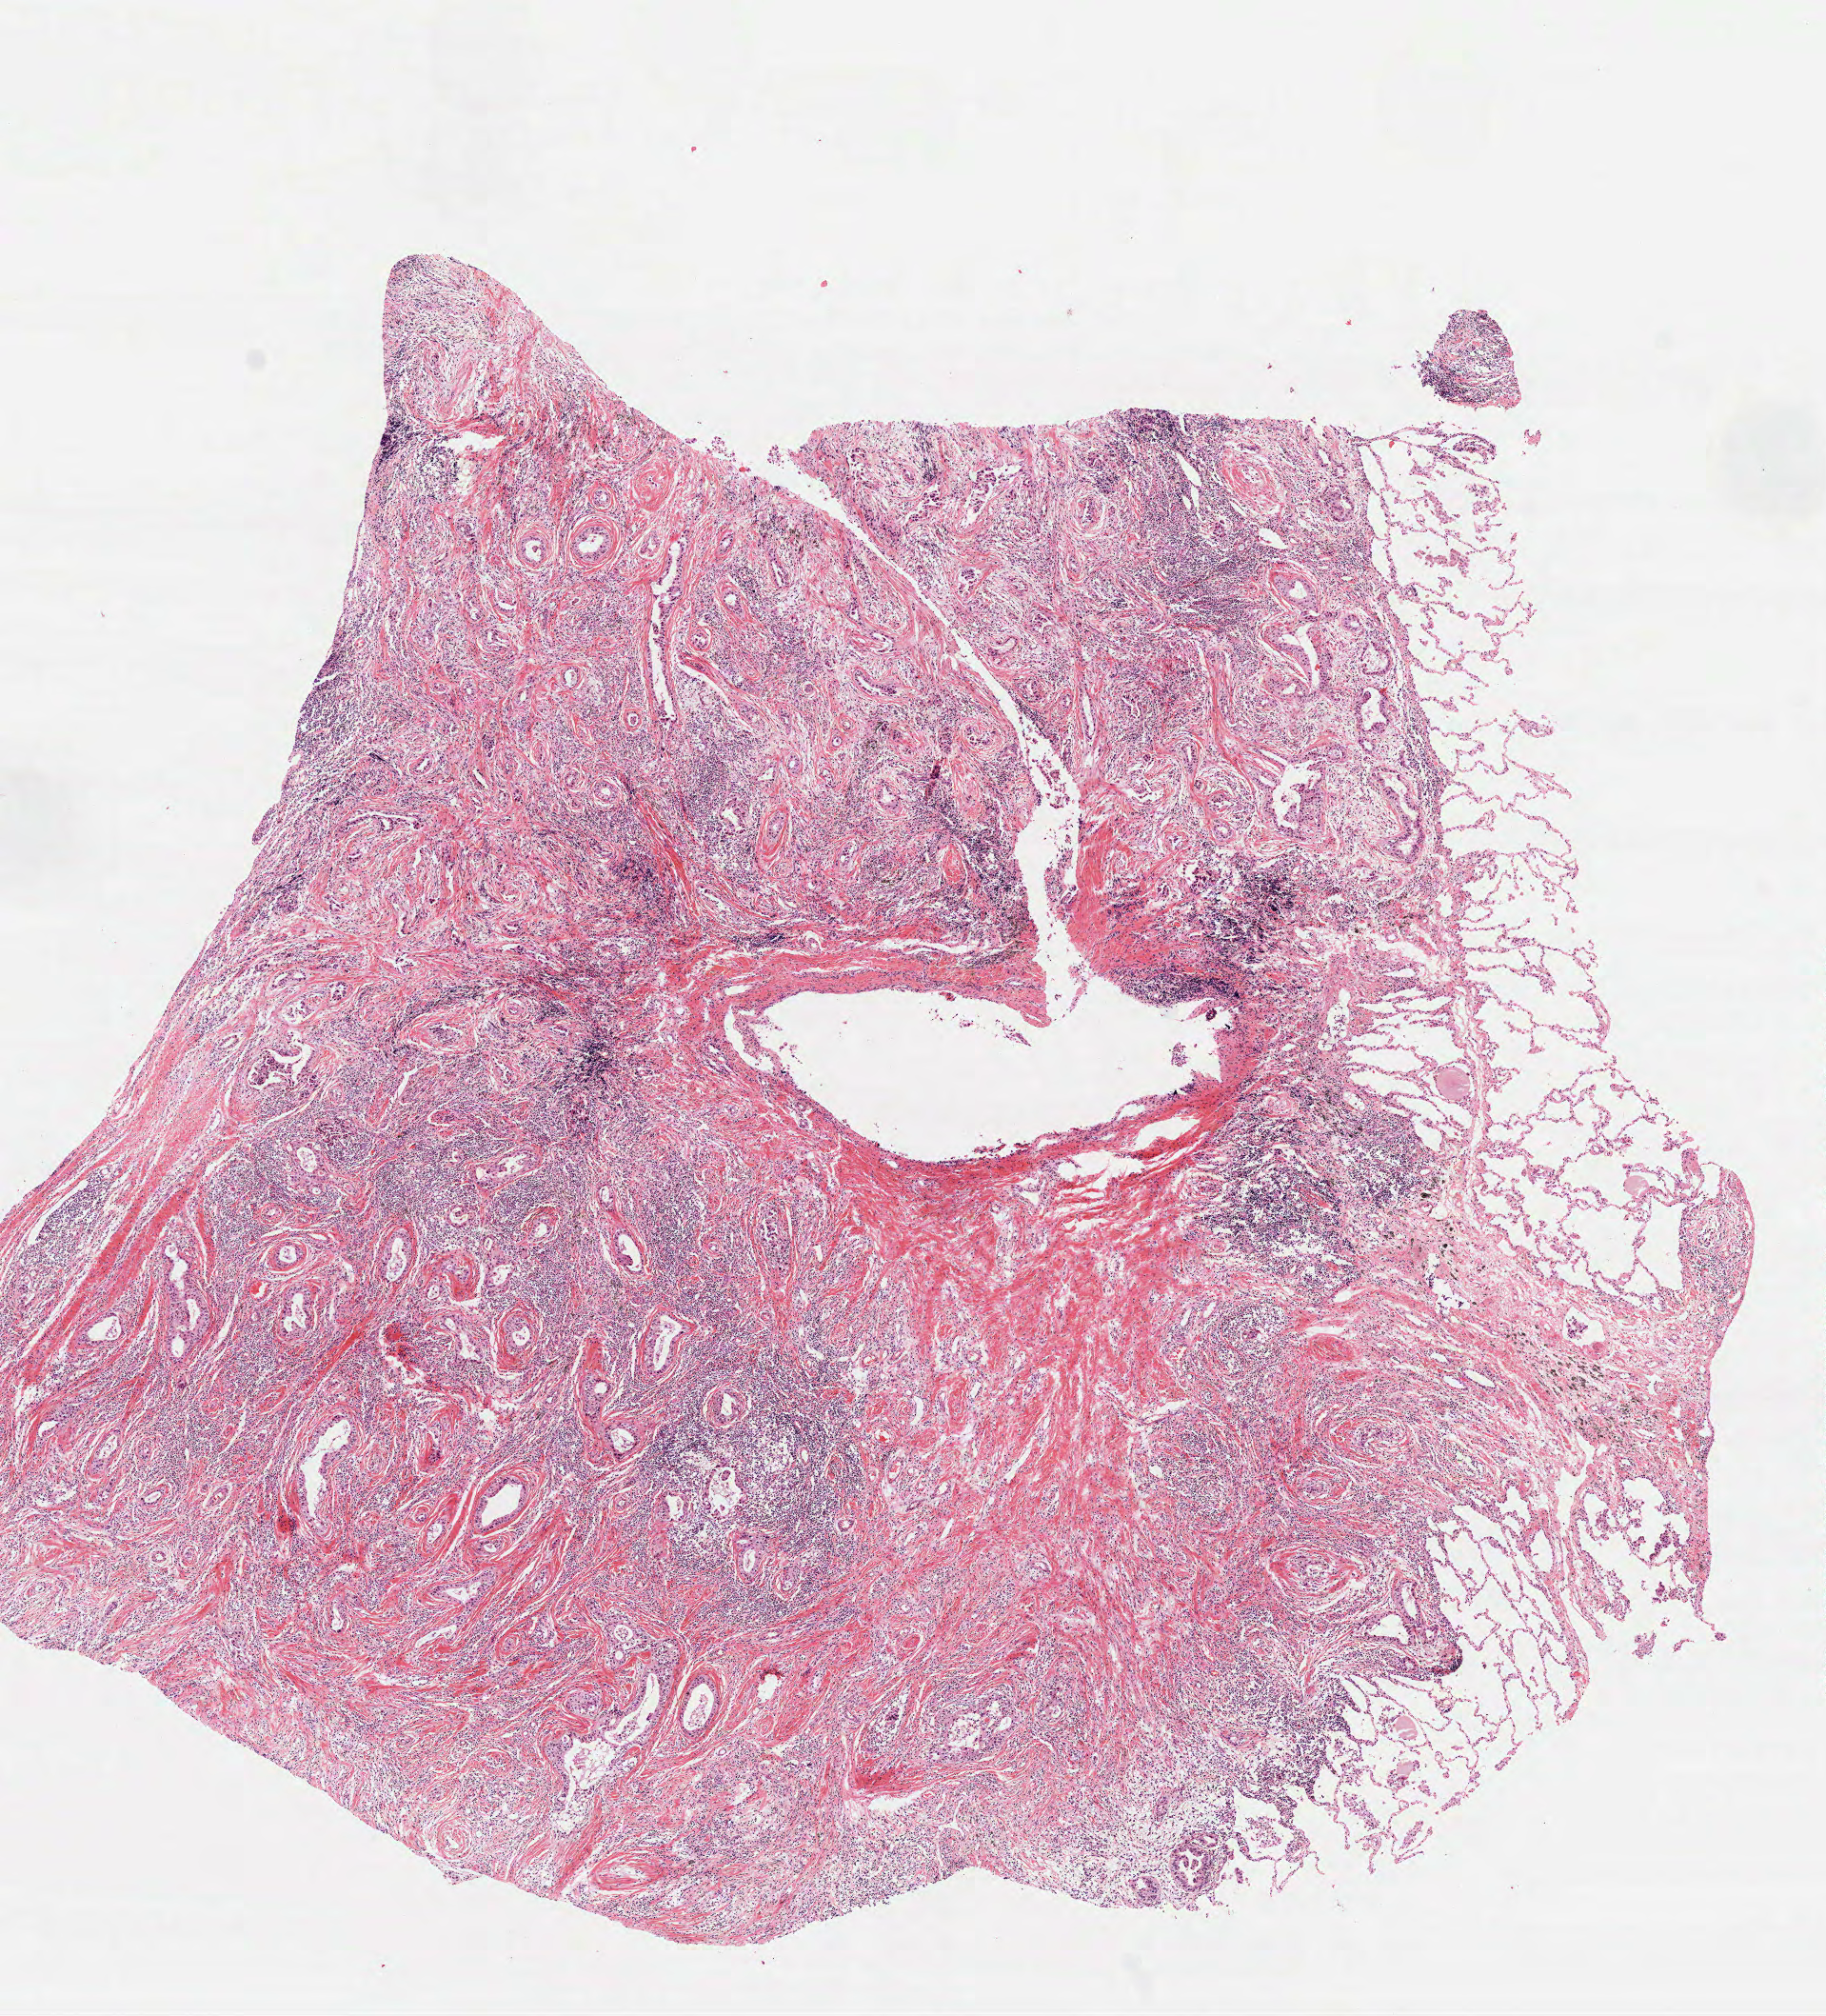
H&E whole-slide image — a low-resolution overview of the entire scanned area, about 7.7 x 8.5 mm; formalin-fixed paraffin-embedded (FFPE) diagnostic section; lung, primary tumour sample. Patient: female, age at initial diagnosis 72 years.
* AJCC pathologic stage: IIB (7th edition)
* laterality: right
* TNM: T2b N1 M0
* pathologic diagnosis: Papillary adenocarcinoma, NOS (upper lobe, lung)